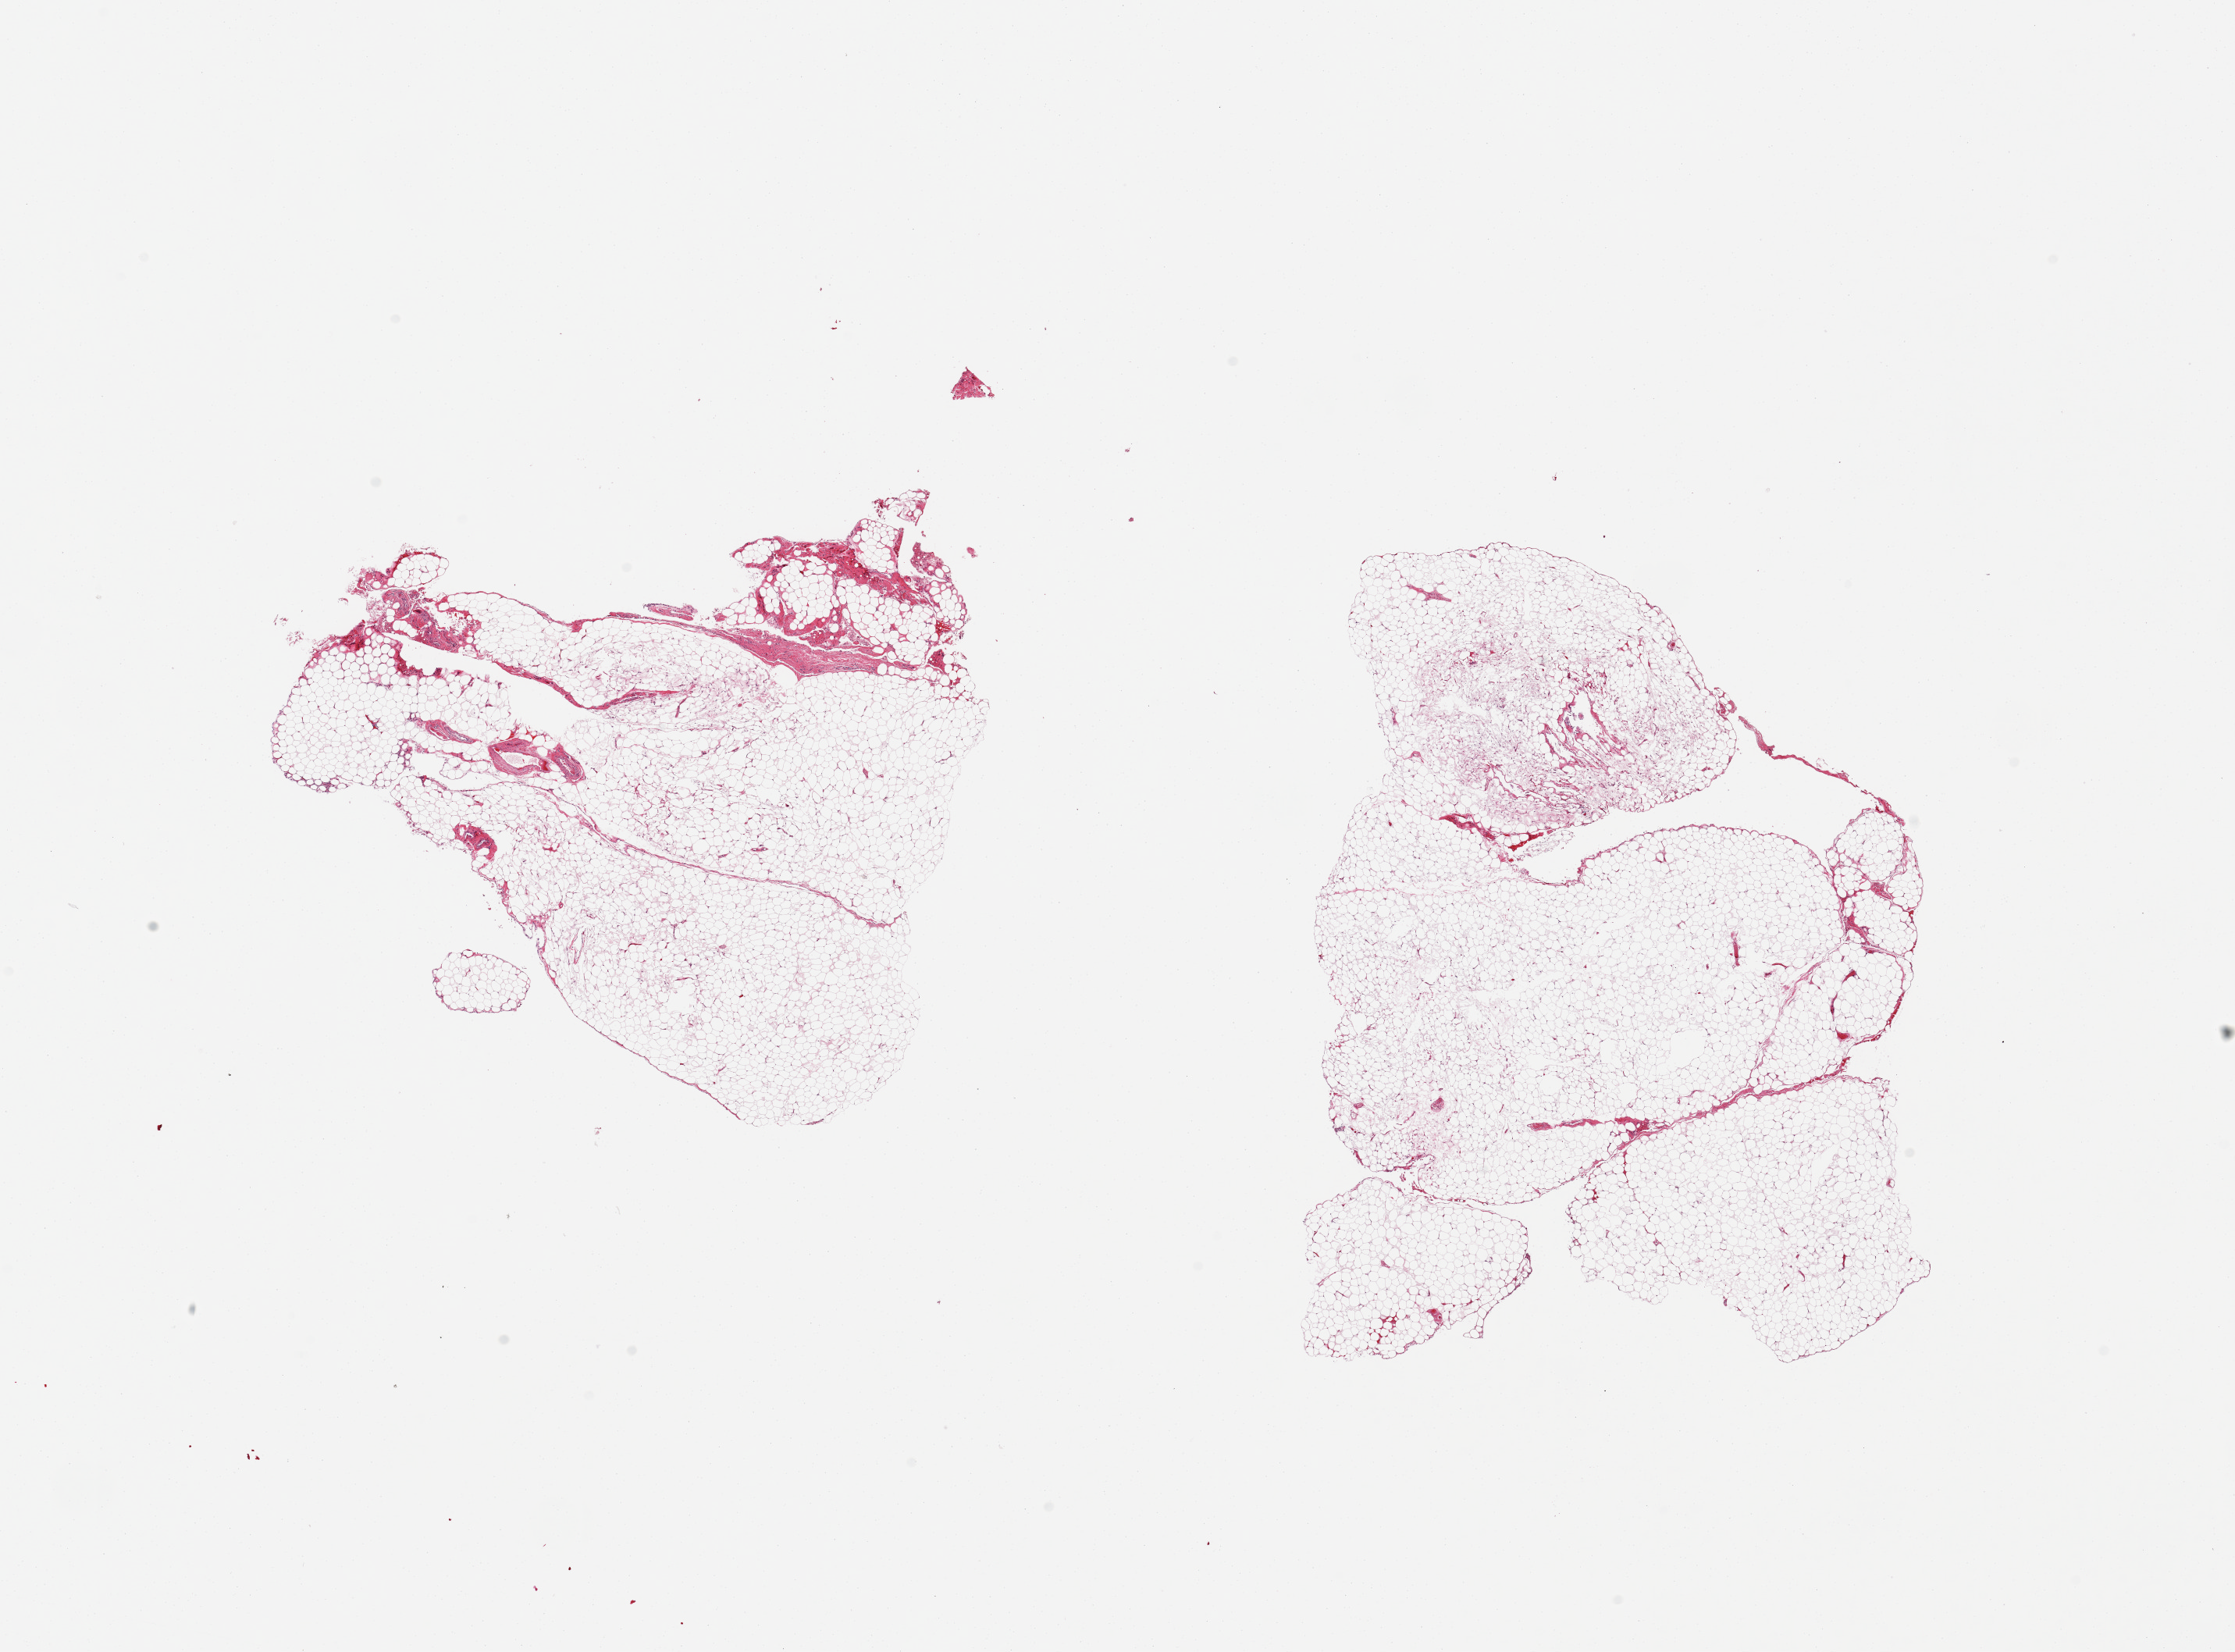
Whole-slide image, haematoxylin and eosin stain, whole scanned area (about 22.6 x 16.7 mm, from a 20x scan) shown as a low-resolution overview, PAXgene-fixed paraffin-embedded (PFPE) section, target tissue: omentum, donor tissue sample. Male donor.
Reviewer comment on this tissue sample: 2 pieces, minimal fascia/vascular elements.